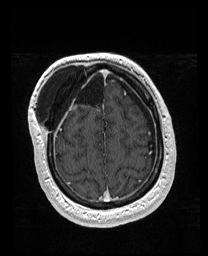
Brain MRI from a brain-tumour surgery series, one axial slice. Position 46 of 176 along the scan axis. T1-weighted post-contrast. 1 mm slice thickness. 208 × 256 image matrix. Case-level facts recorded for this patient, not image findings: histopathology: Astrocytoma; WHO grade: 4; IDH mutation: yes; tumour location: Right Orbitofrontal Anterior Temporal Insular.
Structures marked on this image (manually delineated by an expert):
- previous resection cavity: bounding box (x1, y1, x2, y2) in pixels: (56, 68, 106, 106)